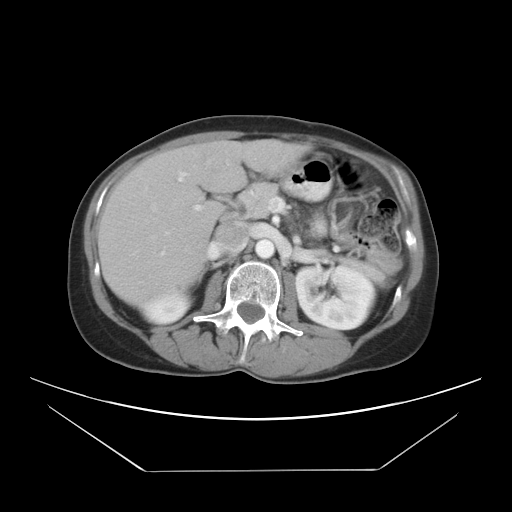
Contrast-enhanced abdominal CT, one axial slice; position 14 of 30 along the scan axis; reconstruction kernel STANDARD; 120 kVp; intravenous contrast given; soft-tissue window (W 400 / L 40 HU); 7.5 mm slice thickness; 512 × 512 image matrix. Female patient, age 54 years. Case-level facts recorded for this patient, not image findings: diagnosis: colorectal cancer liver metastases, imaged before liver resection; multiple liver metastases: yes; largest metastasis: 2.5 cm; chemotherapy before resection: no.
Annotated regions visible in this slice (expert manual segmentation):
- hepatic veins: box from (x=153, y=205) to (x=156, y=211) px
- liver: (x=100, y=140)–(x=298, y=302)
- planned liver remnant (the part of the liver to remain after resection): (x=113, y=142)–(x=248, y=301)
- portal vein (with intrahepatic branches): (x=177, y=169)–(x=200, y=210)